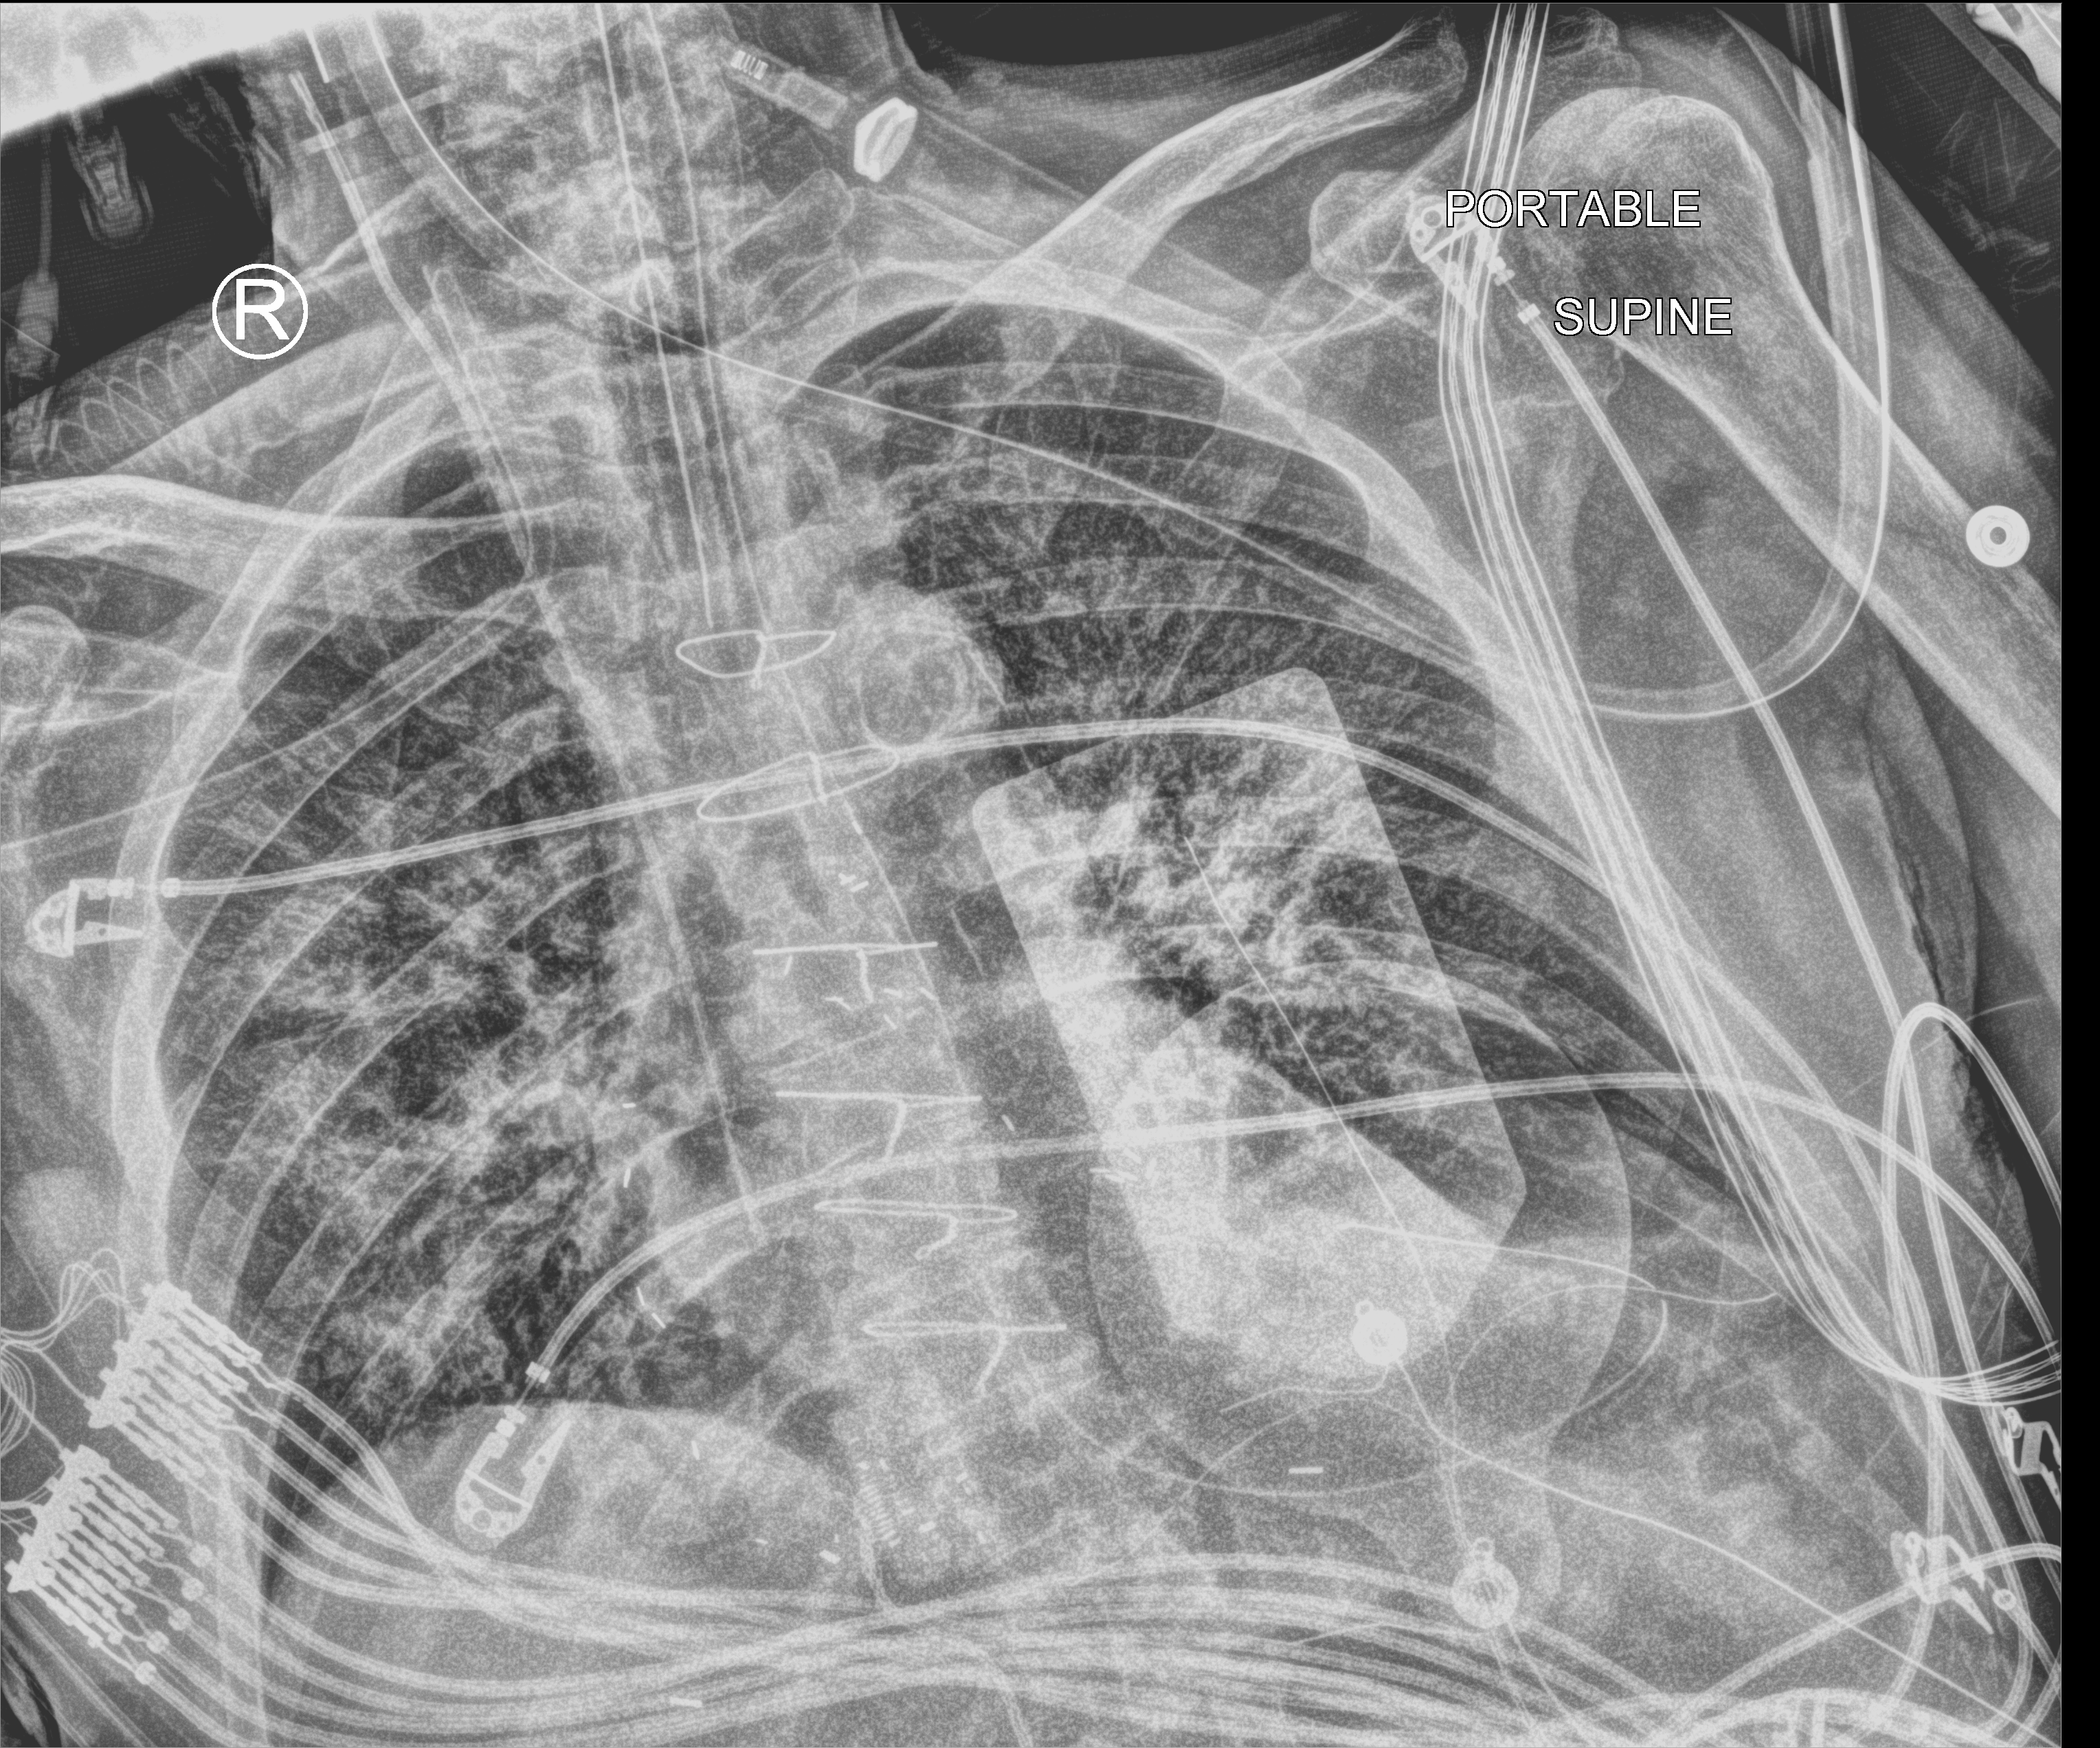
Chest X-ray (portable), anteroposterior (AP) projection. Male patient hospitalised with COVID-19, age 75–90 years.
Hospital-stay facts (about this admission, not read from this image; timing relative to this image not recorded):
- diabetes (admission record): no
- mechanically ventilated during this hospital stay: yes
- COPD (admission record): no